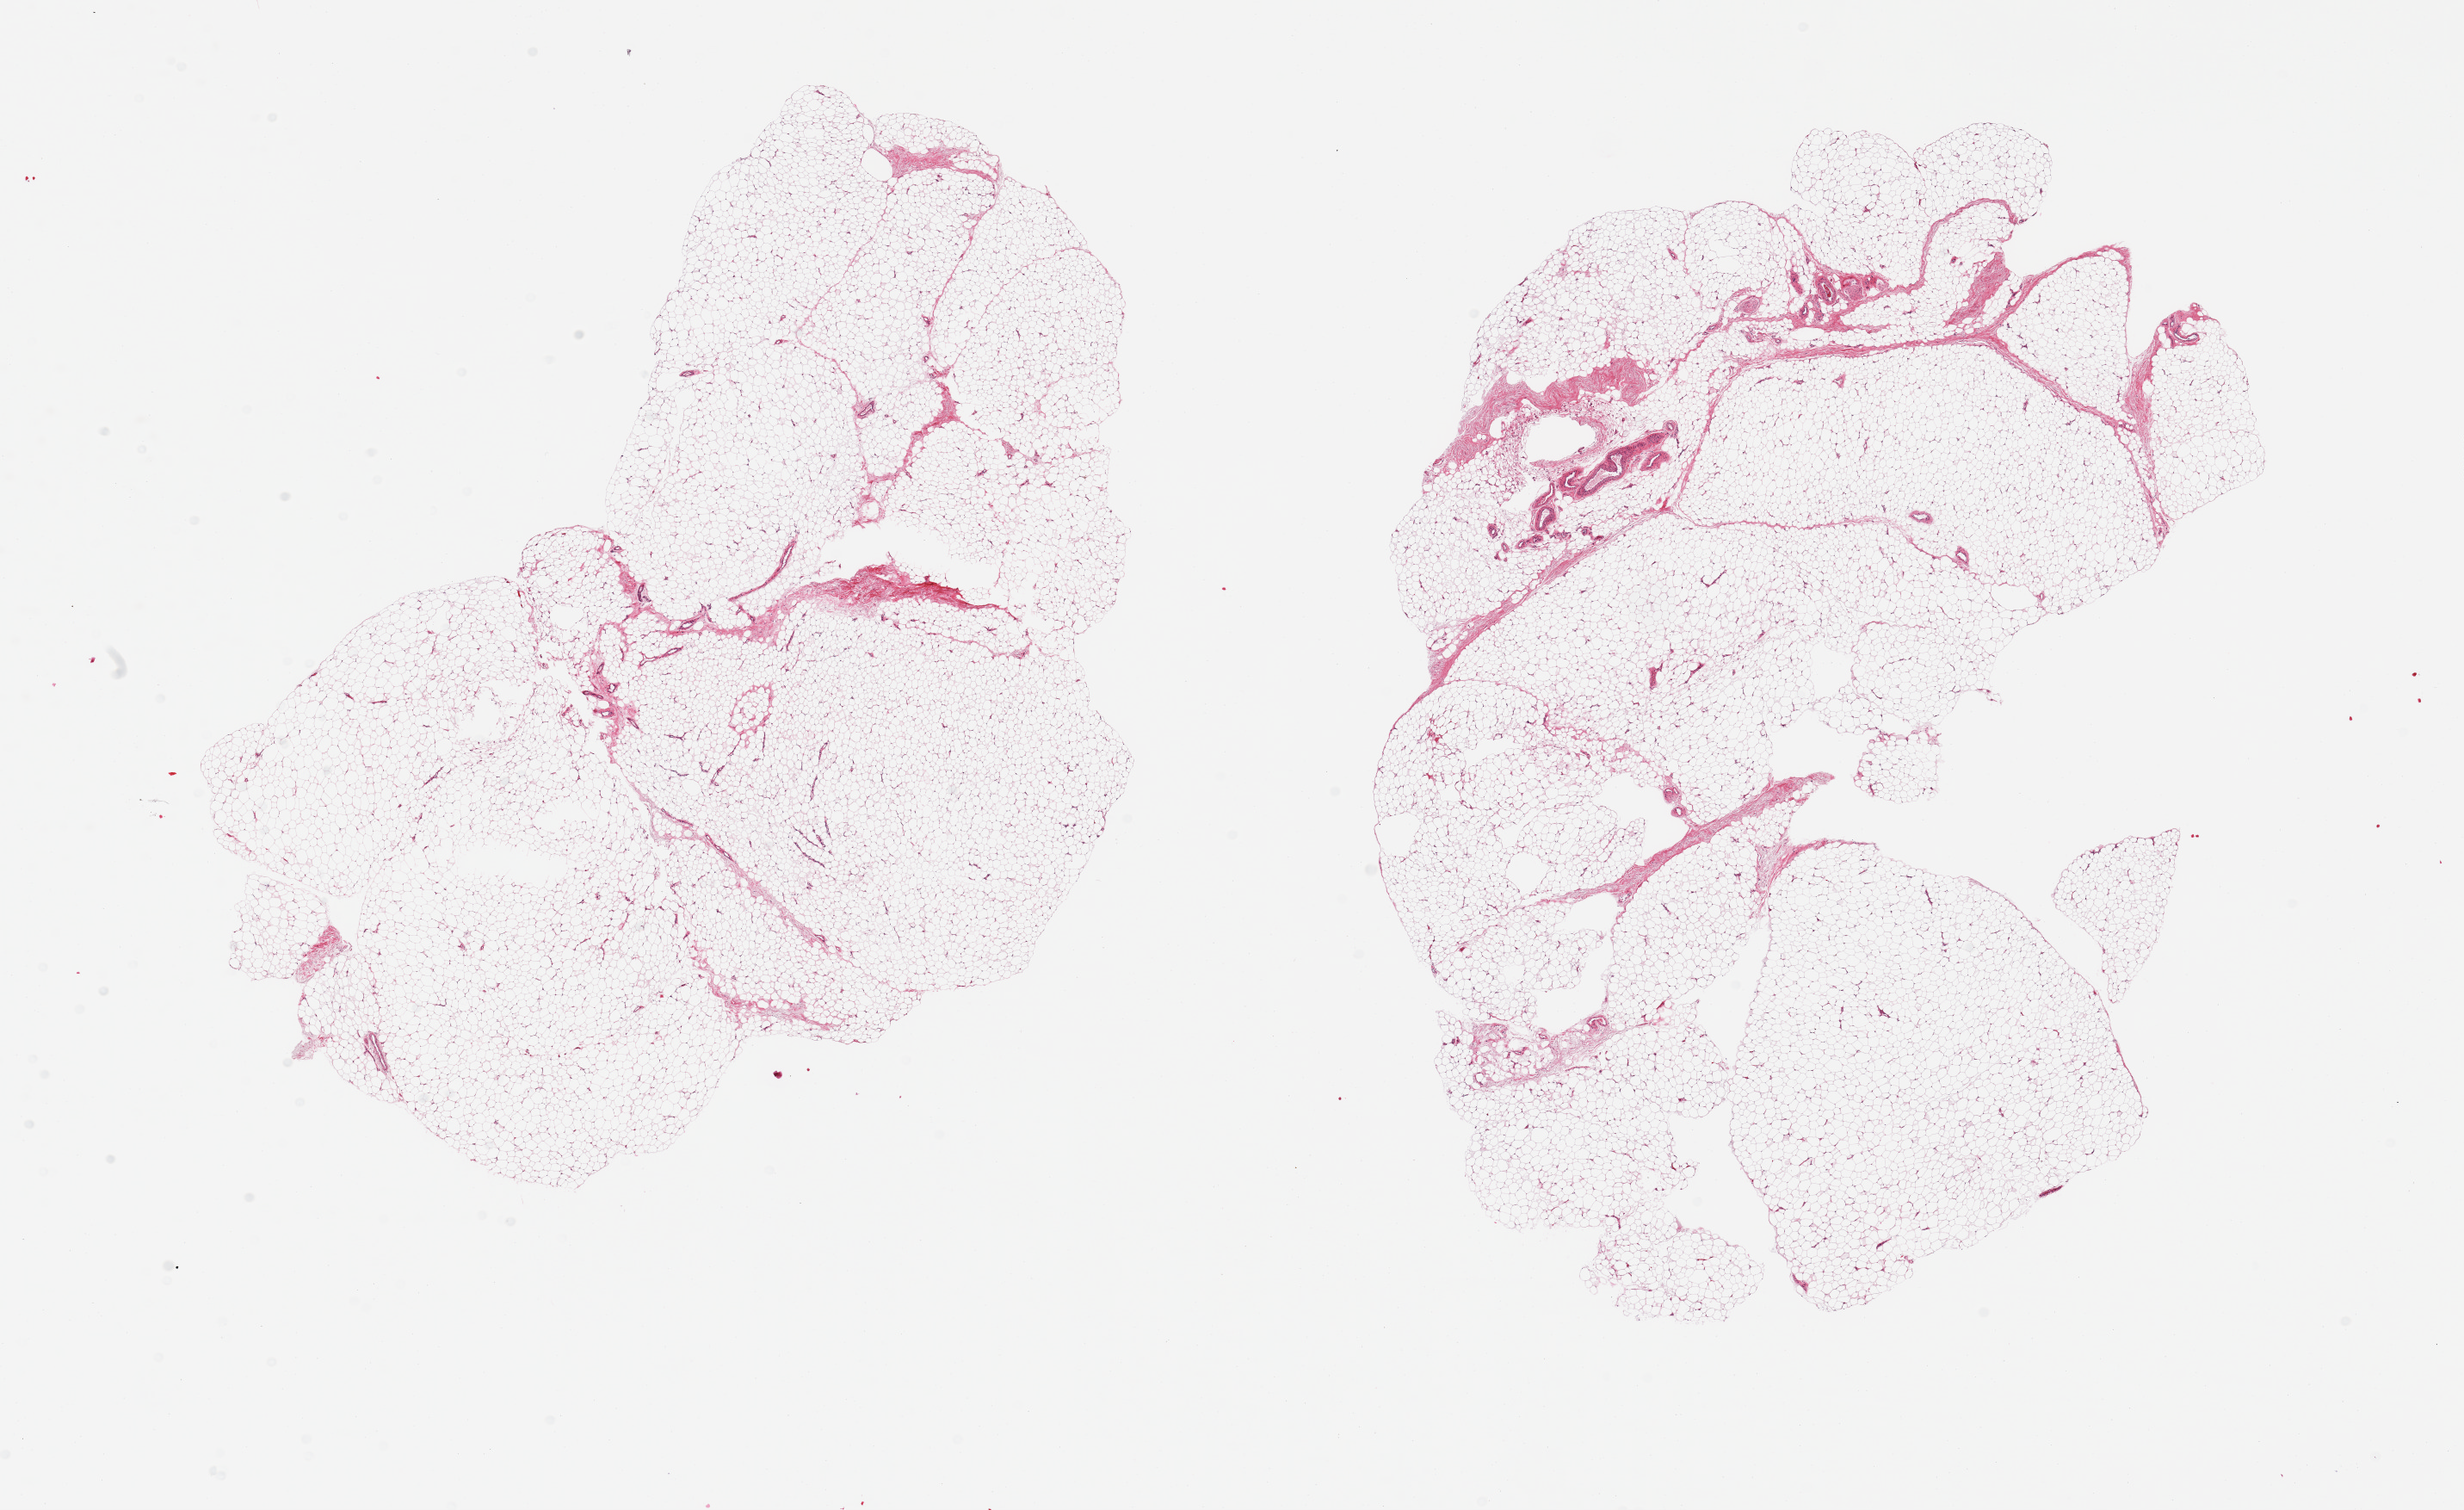
Digitized H&E-stained section, brightfield, a low-resolution overview of the entire scanned area, about 22.6 x 13.9 mm, PAXgene-fixed, paraffin-embedded tissue, sampled site (target tissue): adipose tissue, donor tissue sample. Female donor.
Review note (as recorded): 2 pieces, ~5-10% fascia/vascular elements.